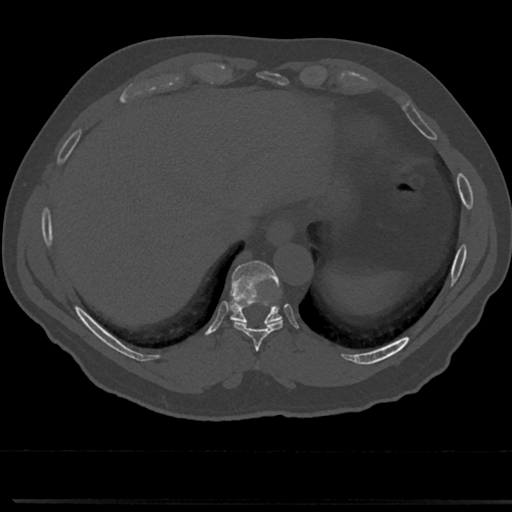
CT including the spine, one axial slice; position 285 of 817 along the scan axis; reconstruction kernel Br40s/3; 120 kVp; bone window (W 1800 / L 400 HU); 0.5 mm slice thickness; 512 × 512 image matrix. Patient: male, 61 years. Case-level facts recorded for this patient, not image findings: primary cancer: prostate.
Annotated regions visible in this slice (semi-automatically segmented with operator editing):
- T8 vertebra: bounding box (x1, y1, x2, y2) in pixels: (255, 352, 263, 372)
- T9 vertebra: (211, 263, 304, 351)